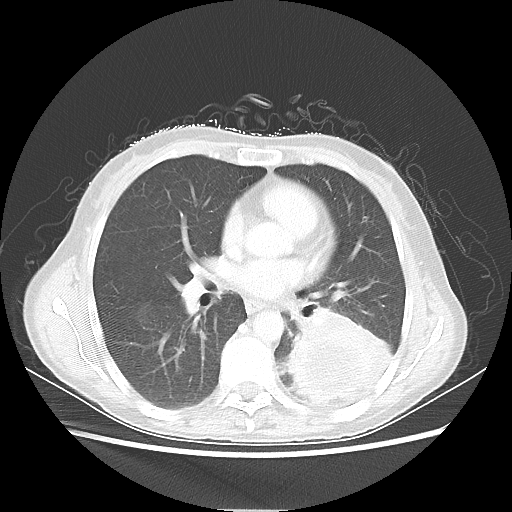
Chest CT, one axial slice; slice 29 of 56 in the series (ordered by position); reconstruction kernel LUNG; 80 kVp; lung window (W 1500 / L -600 HU); 5 mm slice thickness; 512 × 512 image matrix. Patient: female, 53 years. Case-level facts recorded for this patient, not image findings: clinical TNM (as recorded): T3 N0 M0.
Outlined on this slice (bounding box drawn by a radiologist):
- lung tumour (recorded histology: adenocarcinoma): bounding box (x1, y1, x2, y2) in pixels: (287, 309, 392, 407)